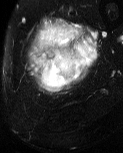
MRI of an extremity soft-tissue mass, one axial slice. Slice 15 of 60 in the series (ordered by position). T2-weighted fat-saturated. MR volume resampled by the dataset authors to the PET/CT grid (not the native acquisition matrix). 3.27 mm slice thickness. 123 × 153 image matrix, field of view 120 × 149 mm. Male patient. Case-level facts recorded for this patient, not image findings: histological type: pleiomorphic liposarcoma; grade: high; site of the primary tumour: left thigh.
Annotated regions visible in this slice (expert contour drawn on MRI and transferred to this co-registered scan by the dataset authors):
- gross tumour volume including surrounding oedema: bounding box [x1, y1, x2, y2] px = [29, 17, 98, 94]
- gross tumour volume (mass): [36, 54, 82, 89]